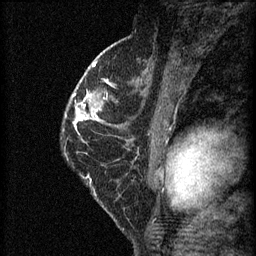
Breast MRI (dynamic contrast-enhanced), one sagittal slice; position 37 of 60 along the scan axis; 3 images stored at this slice position (order not interpretable as contrast timing); 1.5 T; TE 4.2 ms, TR 8.2 ms; 256 × 256 image matrix, field of view 180 × 180 mm. Female patient, age 45 years.
Structures marked on this image (semi-automatic segmentation, software-assisted and operator-edited):
- analysis volume of interest (the breast-tissue region the enhancement analysis was run in; not a lesion): bounding box [x1, y1, x2, y2] px = [64, 98, 104, 135]
- tumour enhancement mask (voxels above the 70 % enhancement threshold inside the analysis volume of interest): [76, 102, 99, 129]